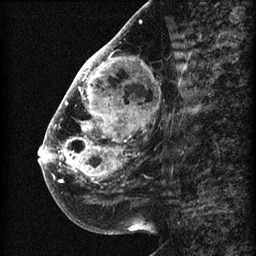
Breast MRI (dynamic contrast-enhanced), one sagittal slice. Position 27 of 60 along the scan axis. 3 images stored at this slice position (order not interpretable as contrast timing). 1.5 T. TE 4.2 ms, TR 22.7 ms. 2 mm slice thickness. 256 × 256 image matrix. Patient: female, 48 years. Case-level facts recorded for this patient, not image findings: setting: breast cancer imaged before/during neoadjuvant chemotherapy; receptor status: triple-negative.
Structures marked on this image (semi-automatic segmentation, software-assisted and operator-edited):
- analysis volume of interest (the breast-tissue region the enhancement analysis was run in; not a lesion): bounding box (x1, y1, x2, y2) in pixels: (44, 30, 173, 207)
- tumour enhancement mask (voxels above the 90 % enhancement threshold inside the analysis volume of interest): (44, 31, 127, 185)